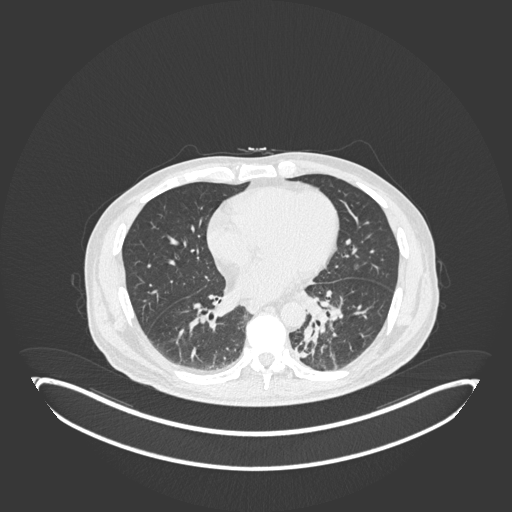
Chest CT, one axial slice; position 66 of 251 along the scan axis; 120 kVp; lung window (W 1500 / L -600 HU); 512 × 512 image matrix. Male patient, age 72 years. Case-level facts recorded for this patient, not image findings: clinical TNM (as recorded): T2b N0 M1.
Structures marked on this image (bounding box drawn by a radiologist):
- lung tumour (recorded histology: adenocarcinoma): bounding box [x1, y1, x2, y2] px = [294, 319, 320, 368]